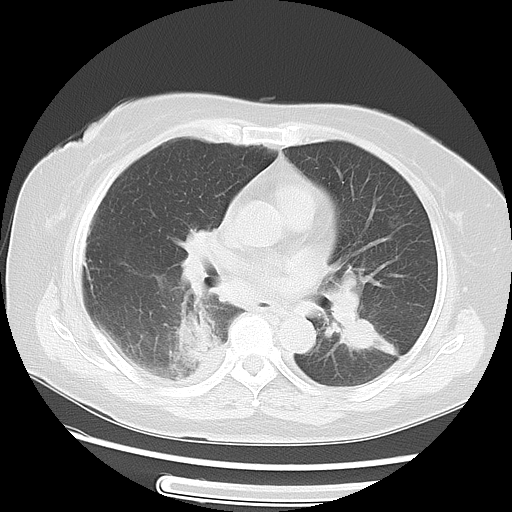
Chest CT, one axial slice. Position 32 of 57 along the scan axis. Reconstruction kernel LUNG. 120 kVp. Lung window (W 1500 / L -600 HU). 5 mm slice thickness. 512 × 512 image matrix, field of view 350 × 350 mm. Female patient, age 69 years. Case-level facts recorded for this patient, not image findings: clinical TNM (as recorded): T2 N1 M1a.
Structures marked on this image (rectangle marked by the reading radiologist):
- lung tumour (recorded histology: adenocarcinoma): bounding box [x1, y1, x2, y2] px = [175, 298, 227, 384]